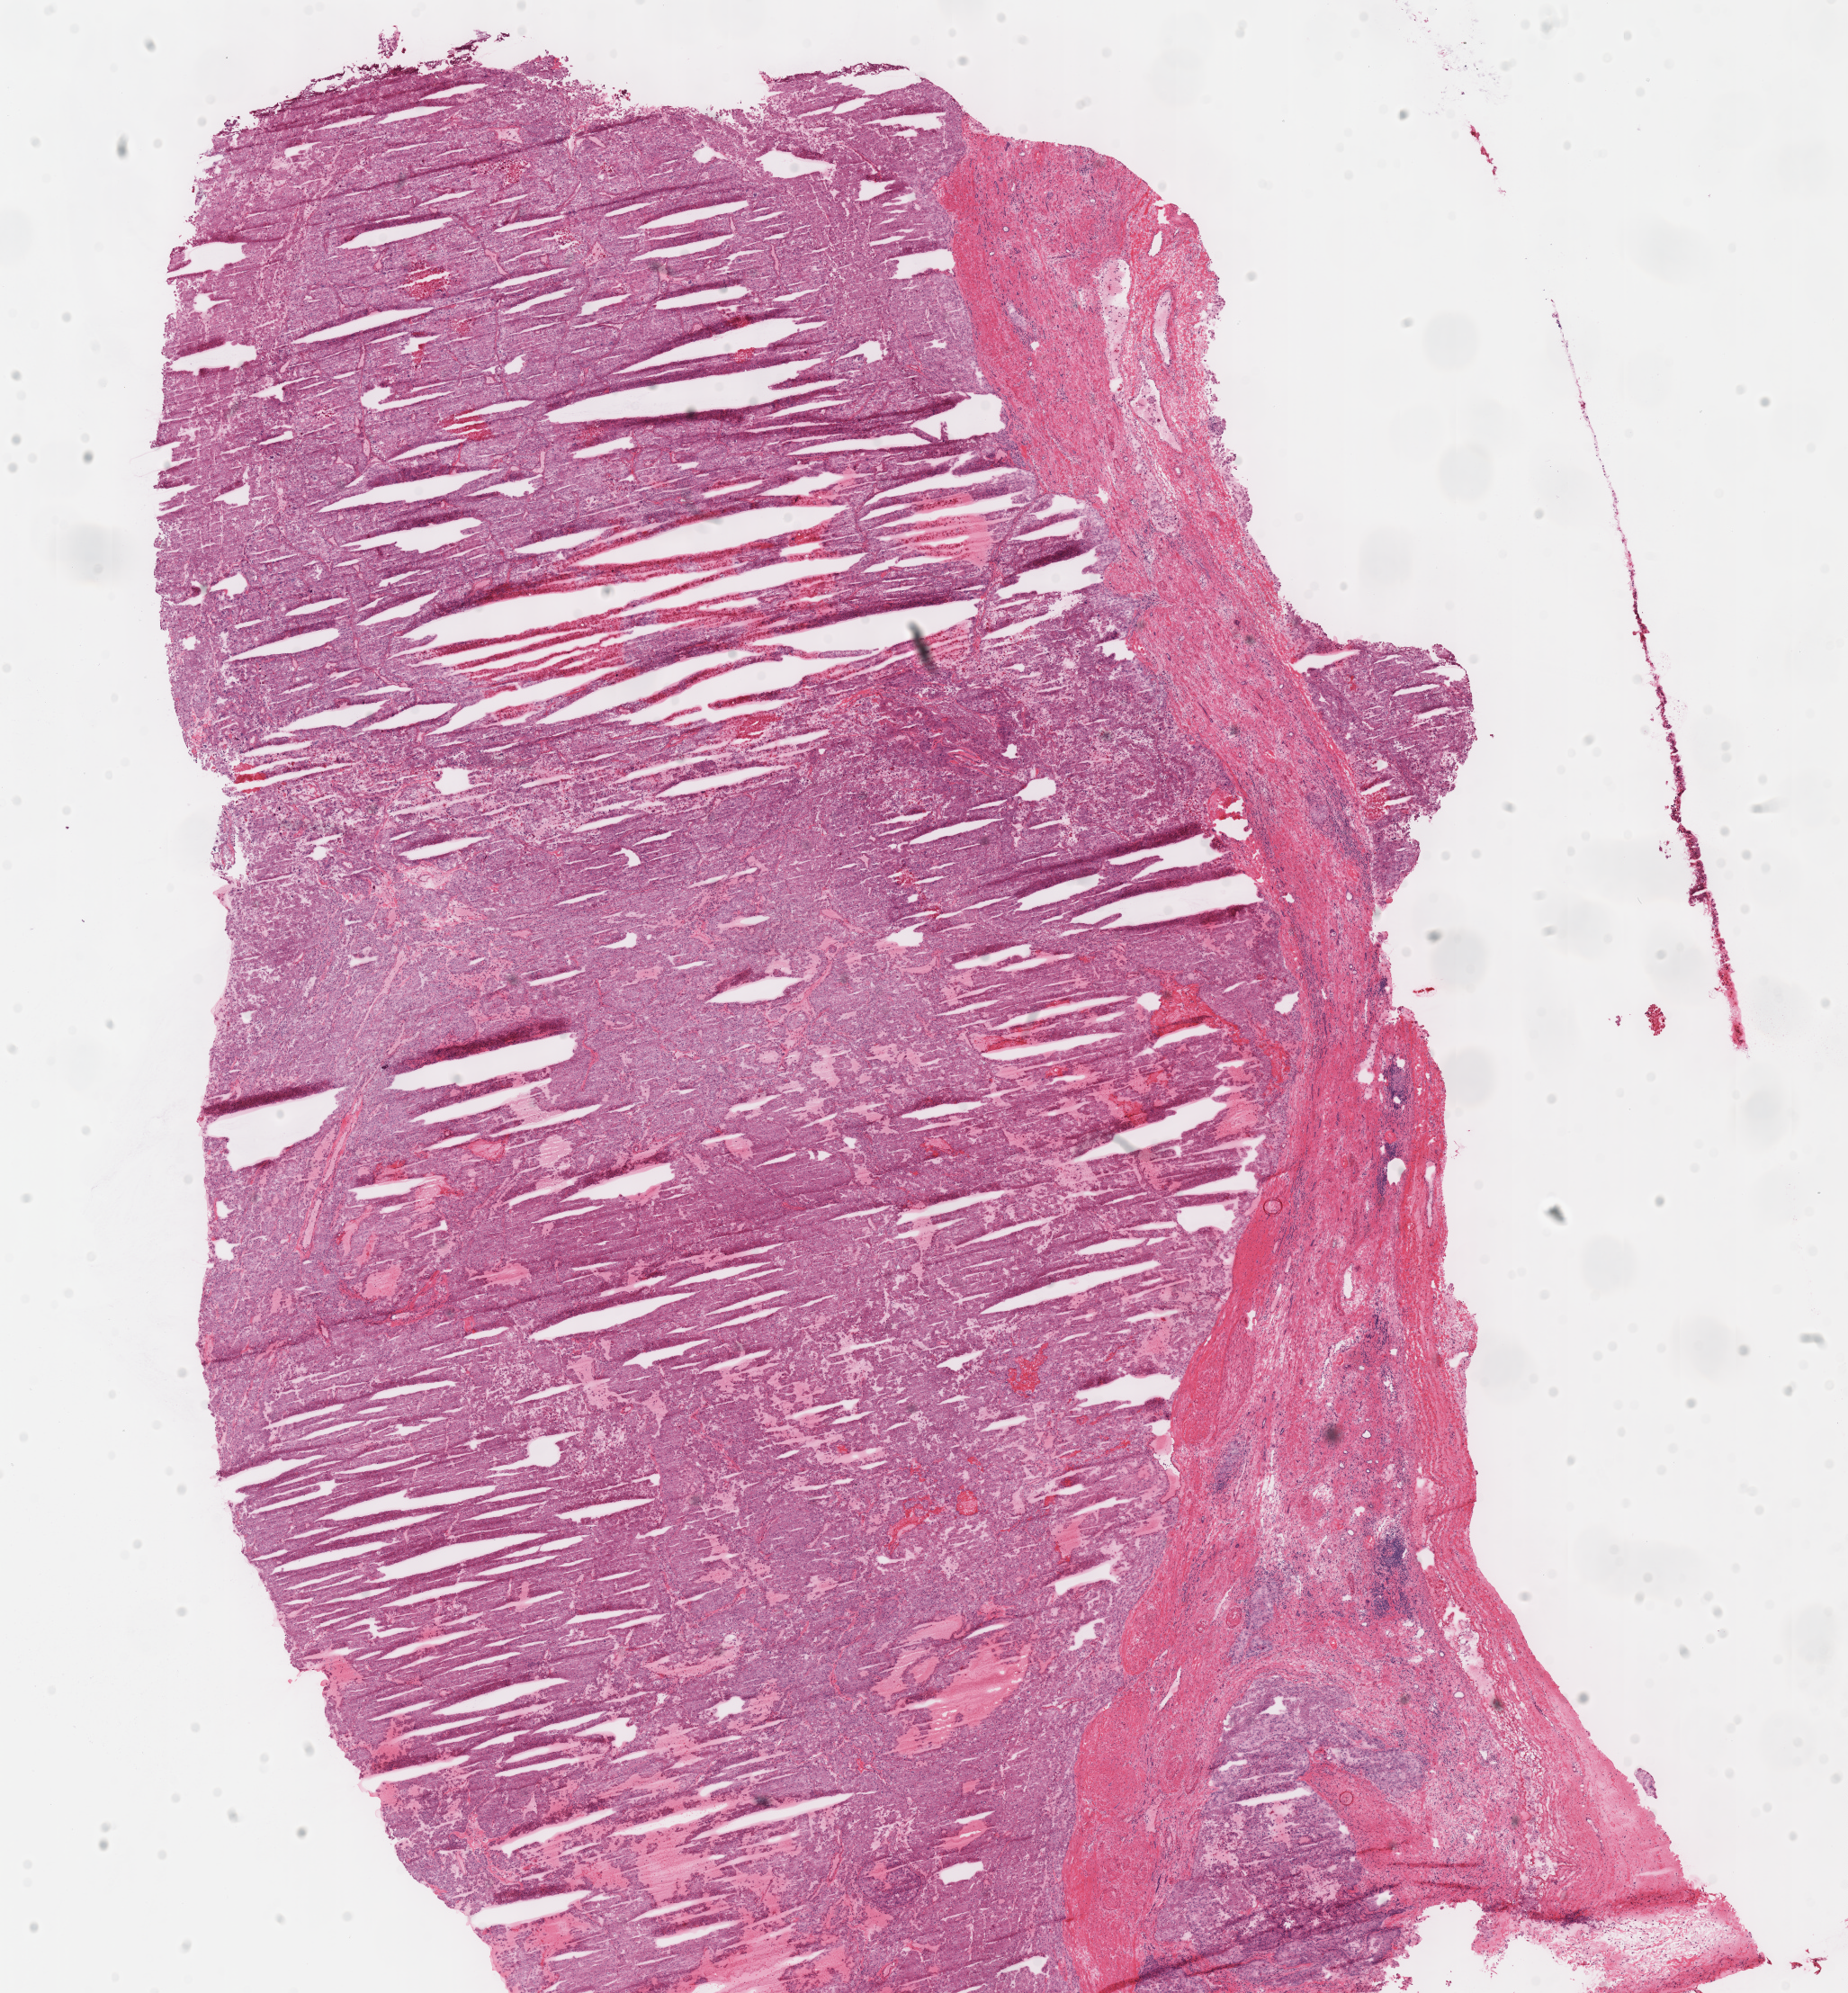
Digitized H&E tissue section (whole slide) — a low-resolution overview of the entire scanned area, about 16.2 x 17.4 mm; frozen section; kidney, primary tumour sample. Patient: female, age at initial diagnosis 51 years. Slide review estimates, as recorded: tumour cells 85%, tumour nuclei 80%, normal cells 0%, stromal cells 14%, necrosis 1%. Infiltration values recorded for this section: lymphocyte infiltration 10%, monocyte infiltration 0%, neutrophil infiltration 0%.
Lymph nodes positive (case pathology): 4 of 26 examined. TNM: T3b N2 M0. AJCC pathologic stage: IV (6th edition). Laterality: right. Pathologic diagnosis: Renal cell carcinoma, chromophobe type.